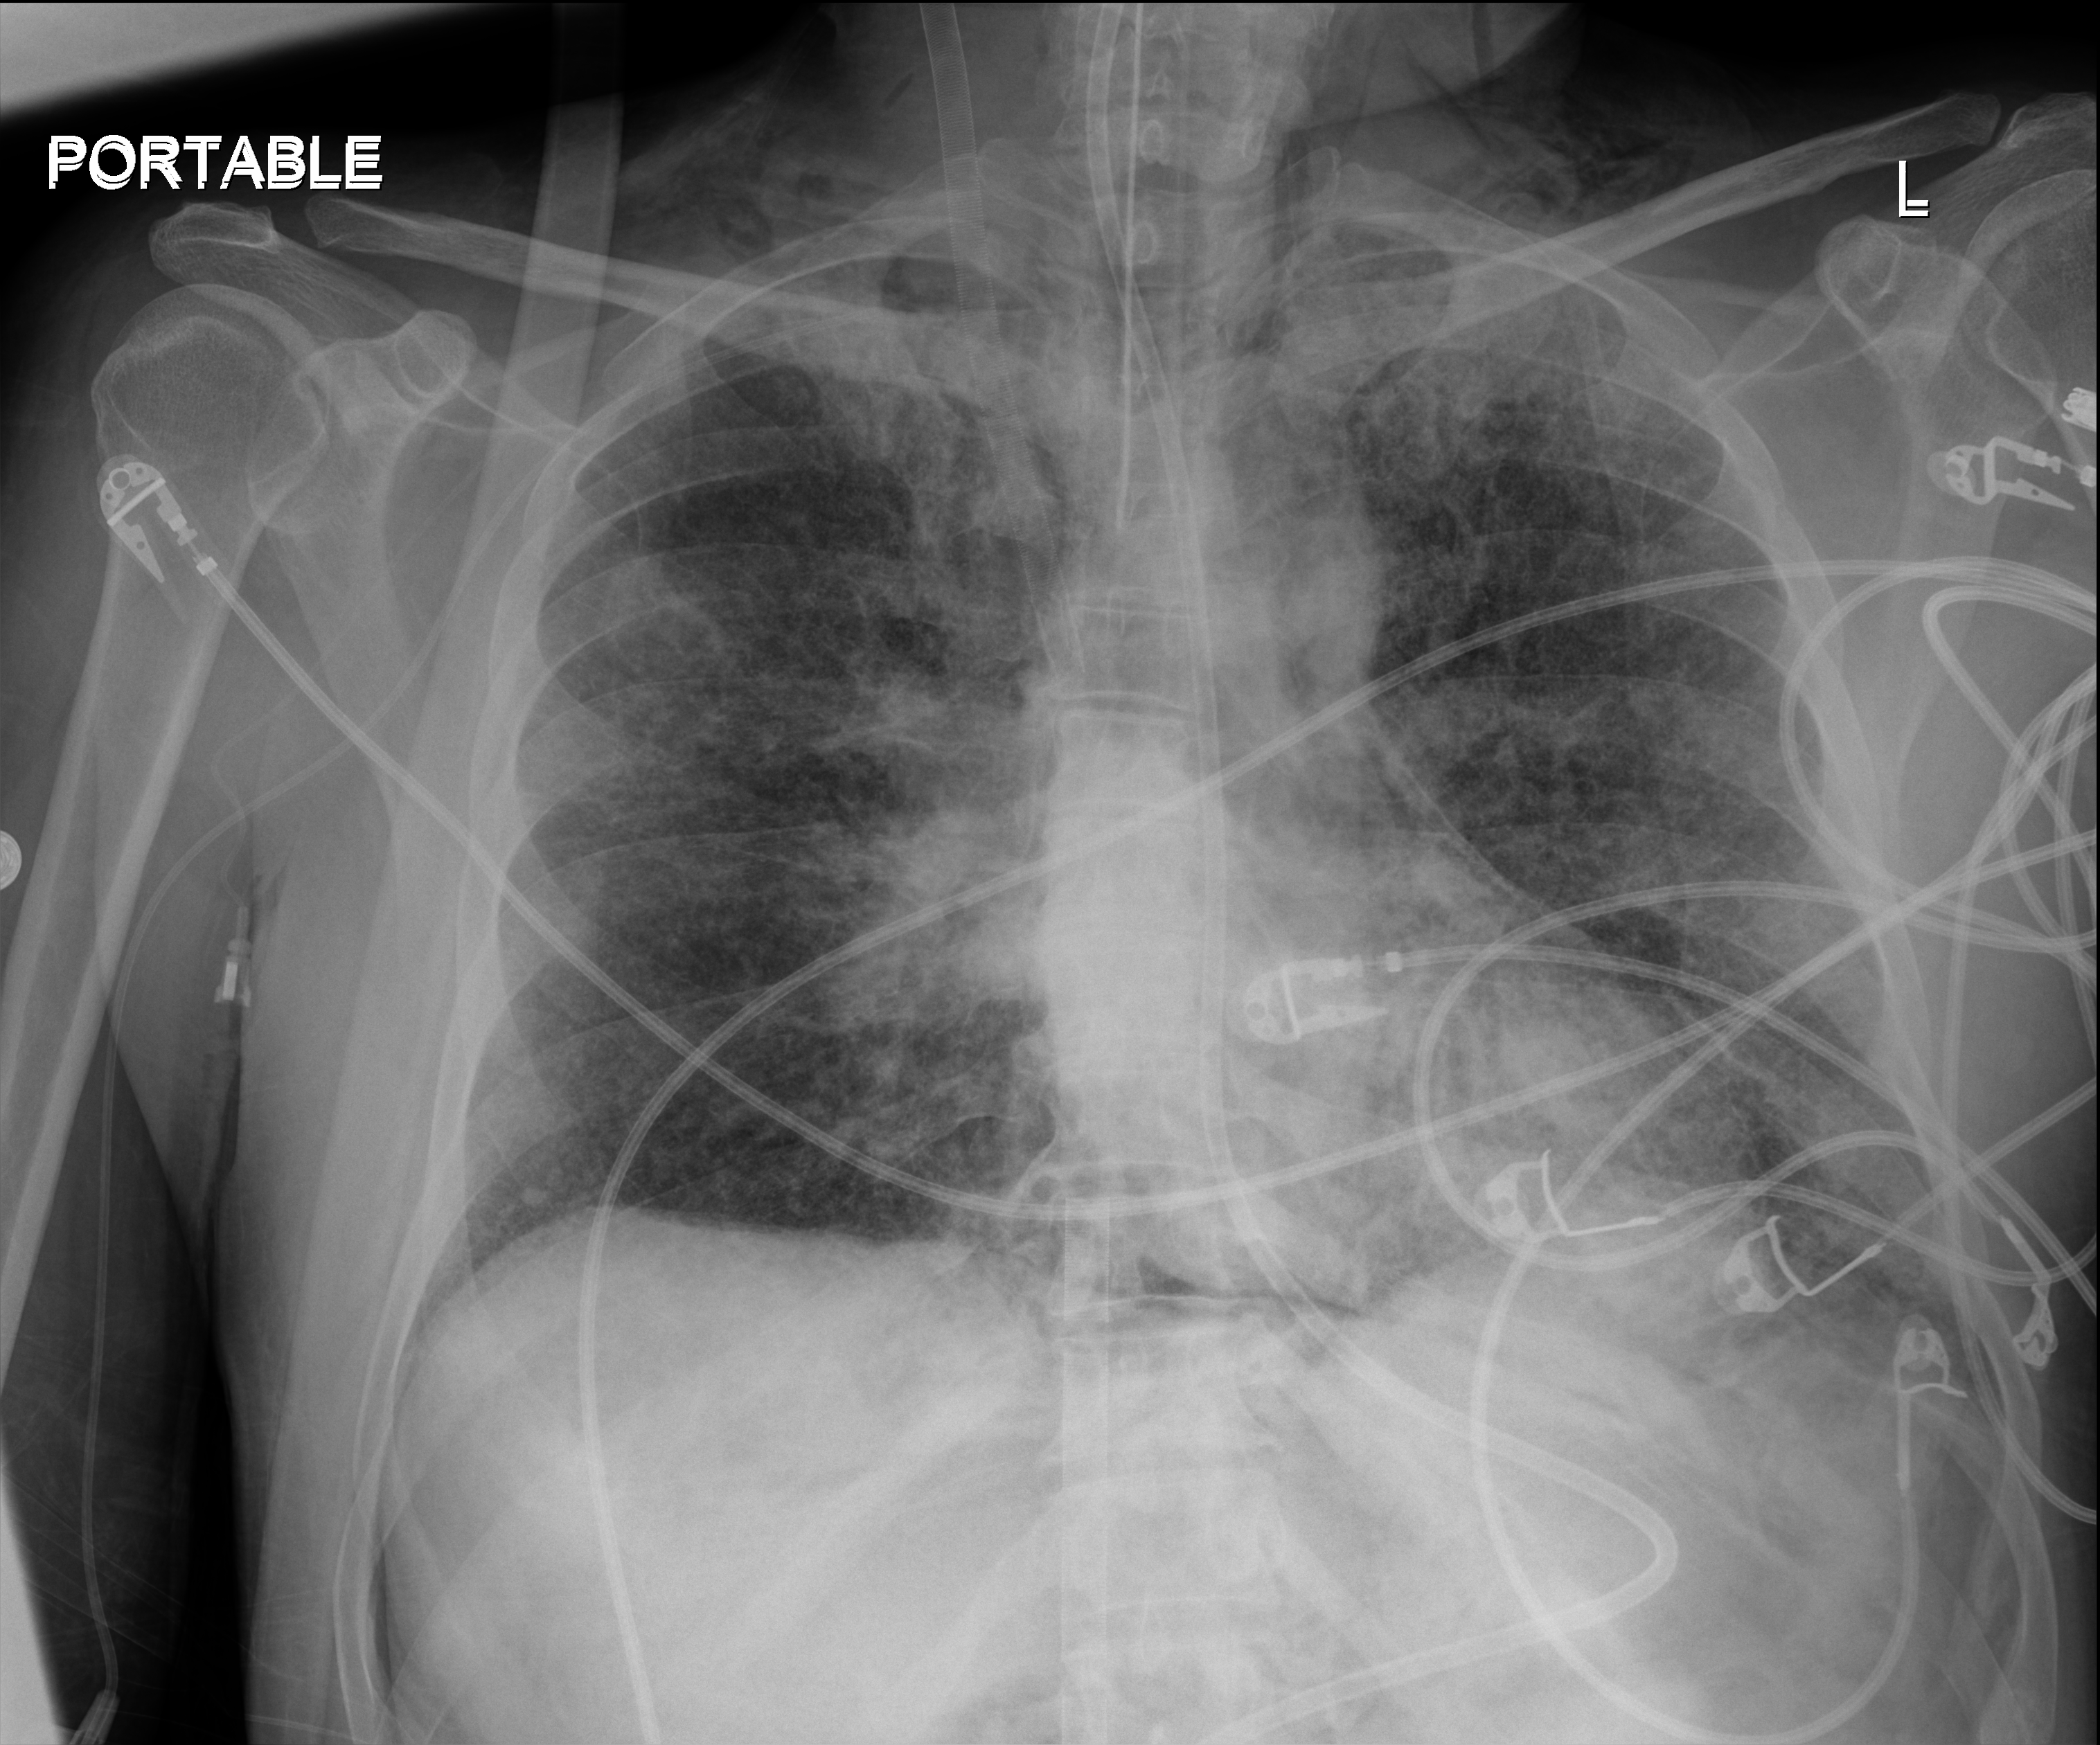
Chest X-ray (portable). Male patient hospitalised with COVID-19, age 18–59 years.
From the hospital-stay record, not from the radiograph (when in the stay this image was taken is not recorded): mechanically ventilated during this hospital stay: yes; chronic kidney disease (admission record): no.